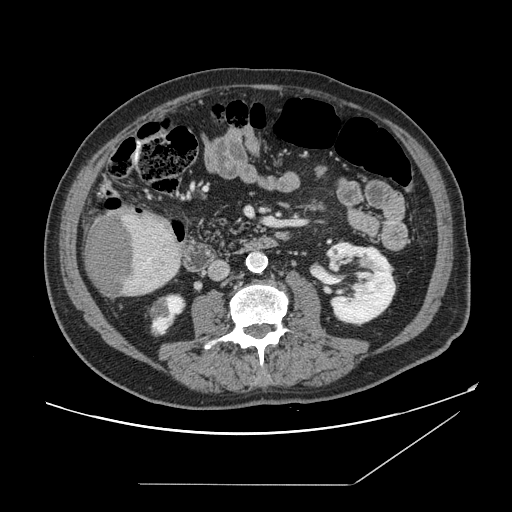
Contrast-enhanced abdominal CT, one axial slice. Position 43 of 166 along the scan axis. Intravenous contrast given. Soft-tissue window (W 400 / L 40 HU). 512 × 512 image matrix, field of view 416 × 416 mm. Male patient, age 80 years. From the clinical record (not read from this slice): diagnosis: colorectal cancer liver metastases, imaged before liver resection; multiple liver metastases: no; largest metastasis: 2.2 cm; disease in both lobes: no.
Outlined on this slice (expert manual segmentation):
- liver: bounding box (x1, y1, x2, y2) in pixels: (85, 208, 181, 298)
- liver metastasis: (86, 212, 135, 297)